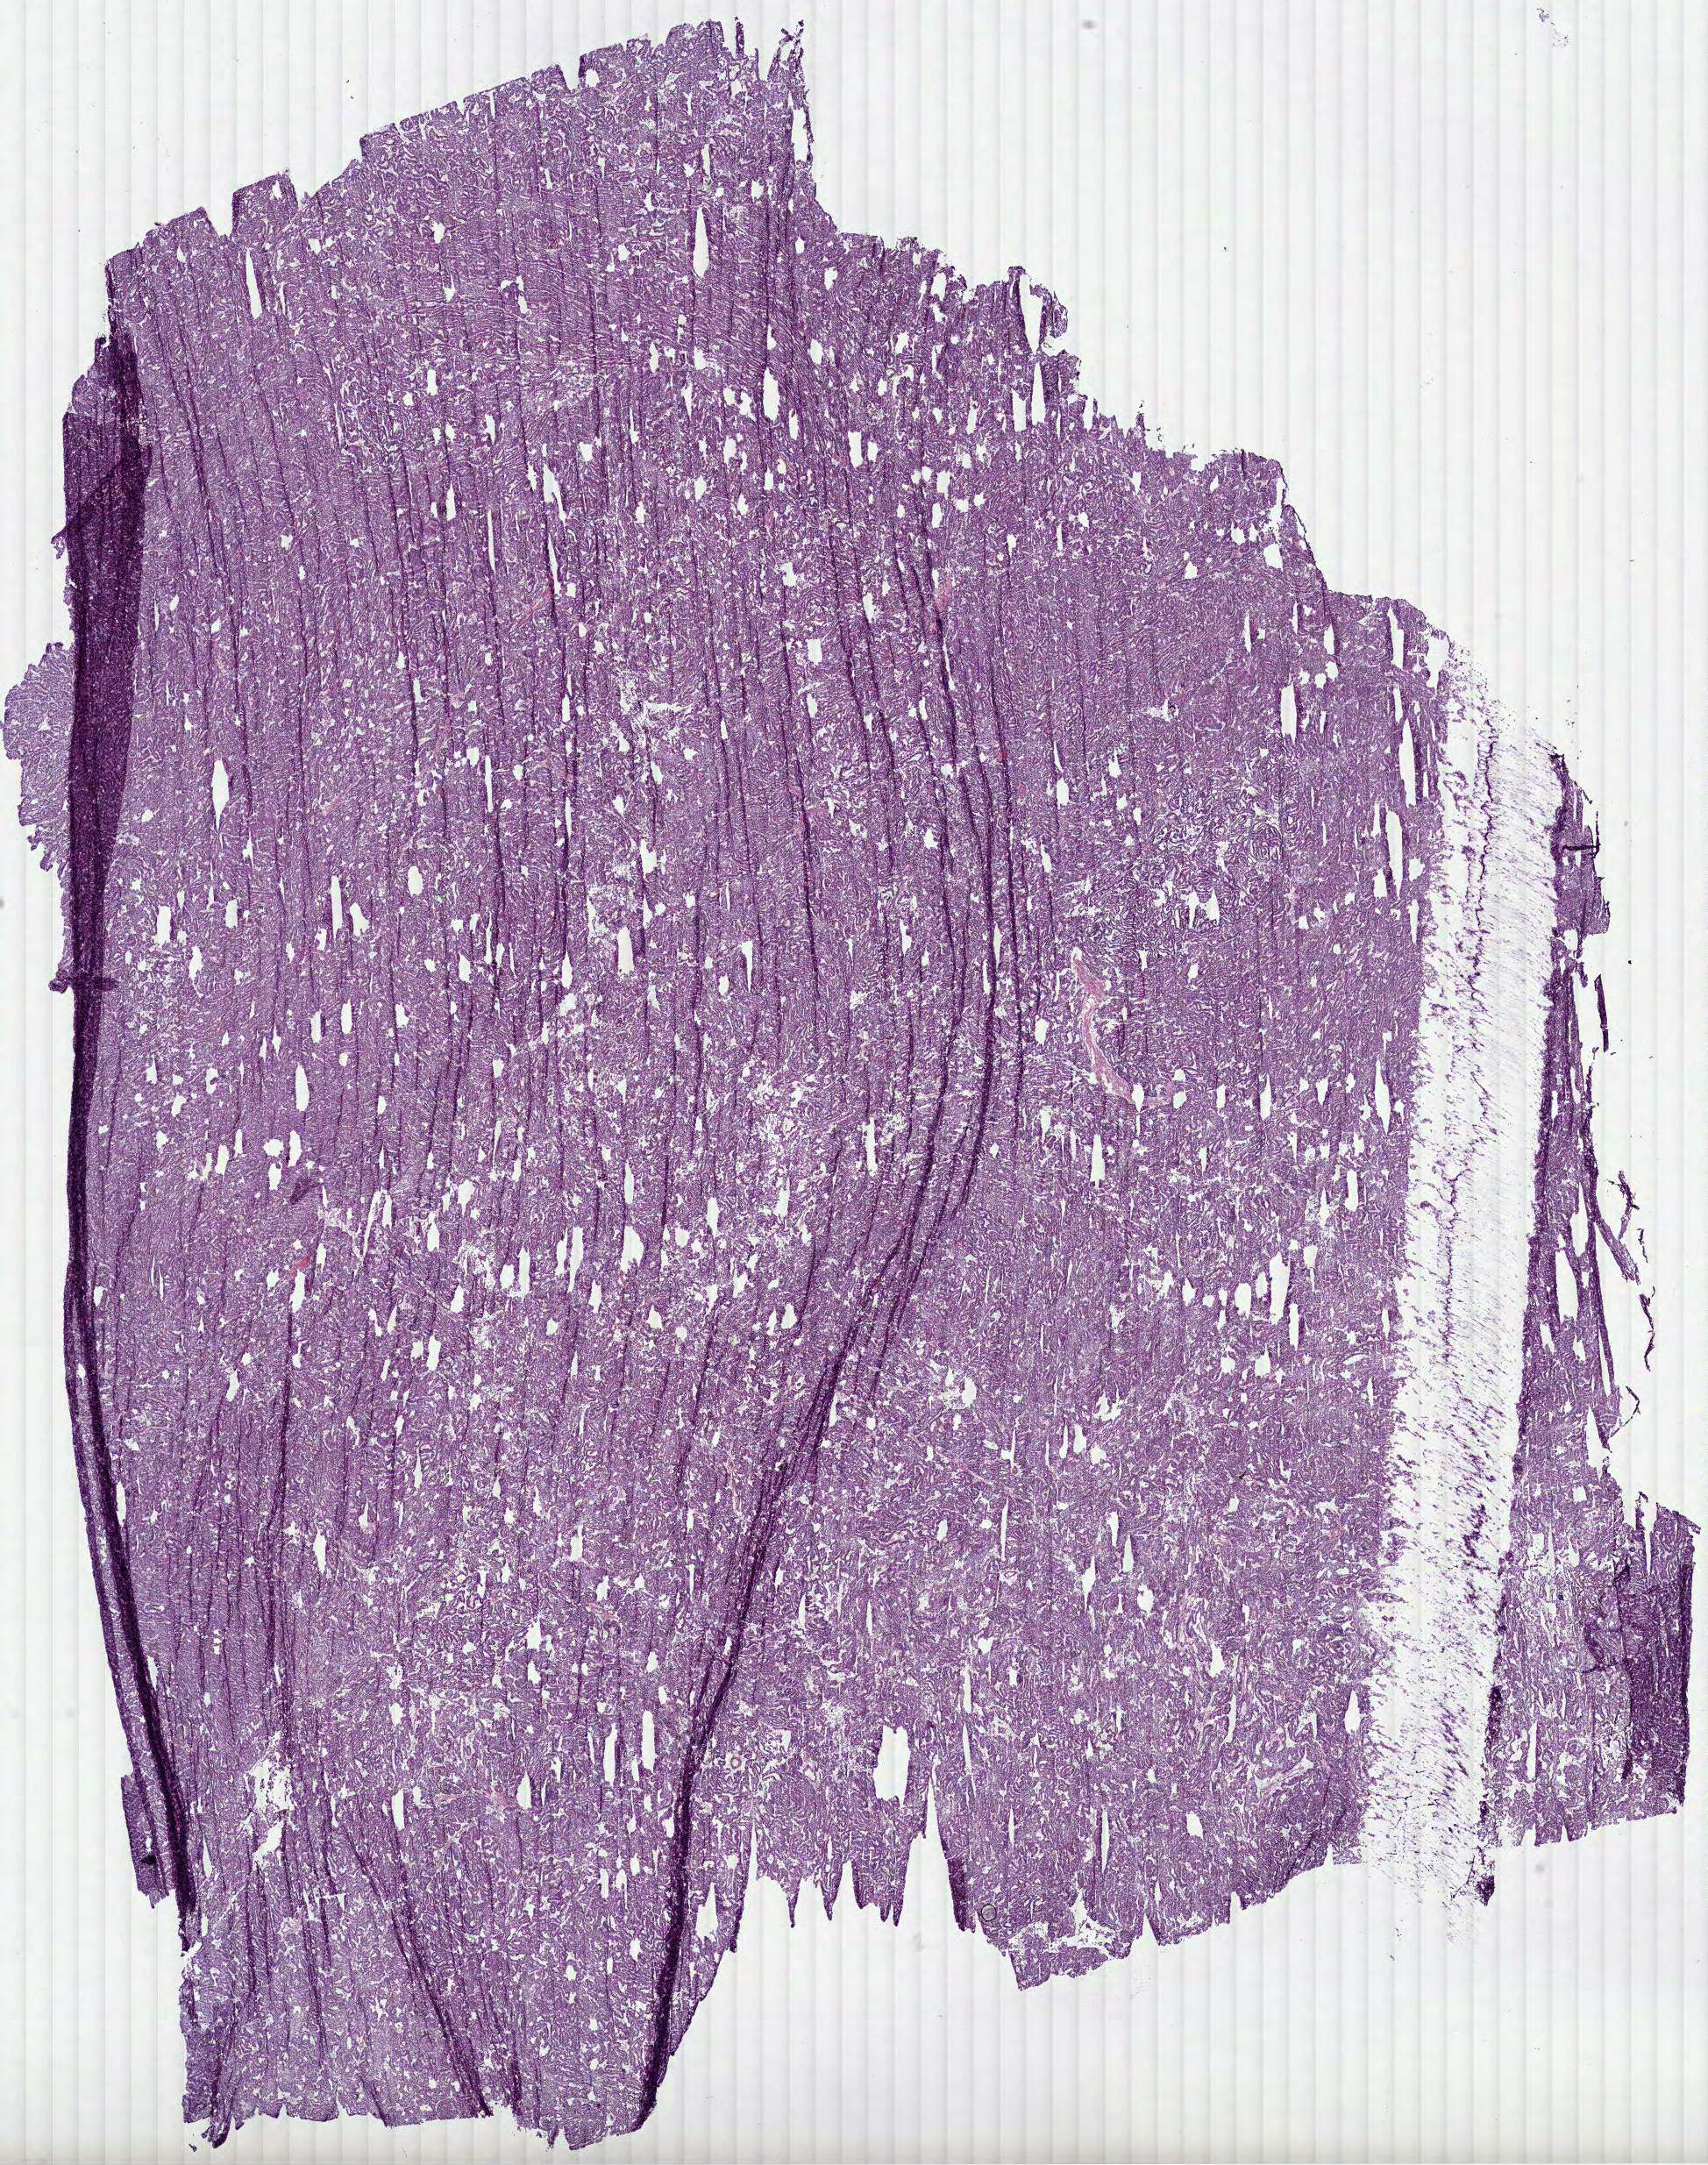
Digitized H&E-stained tissue section (whole slide) — a low-resolution overview of the entire scanned area, about 15.7 x 19.9 mm; frozen section from the bottom of the tissue portion; sample: primary tumour, kidney. Patient: female, age at initial diagnosis 57 years. Pathologist review of this section (percent, as recorded): tumour cells 95%, tumour nuclei 80%, normal cells 0%, stromal cells 5%, necrosis 0%.
- AJCC pathologic stage: III
- TNM: T3b N0 M0
- pathologic diagnosis: Papillary adenocarcinoma, NOS